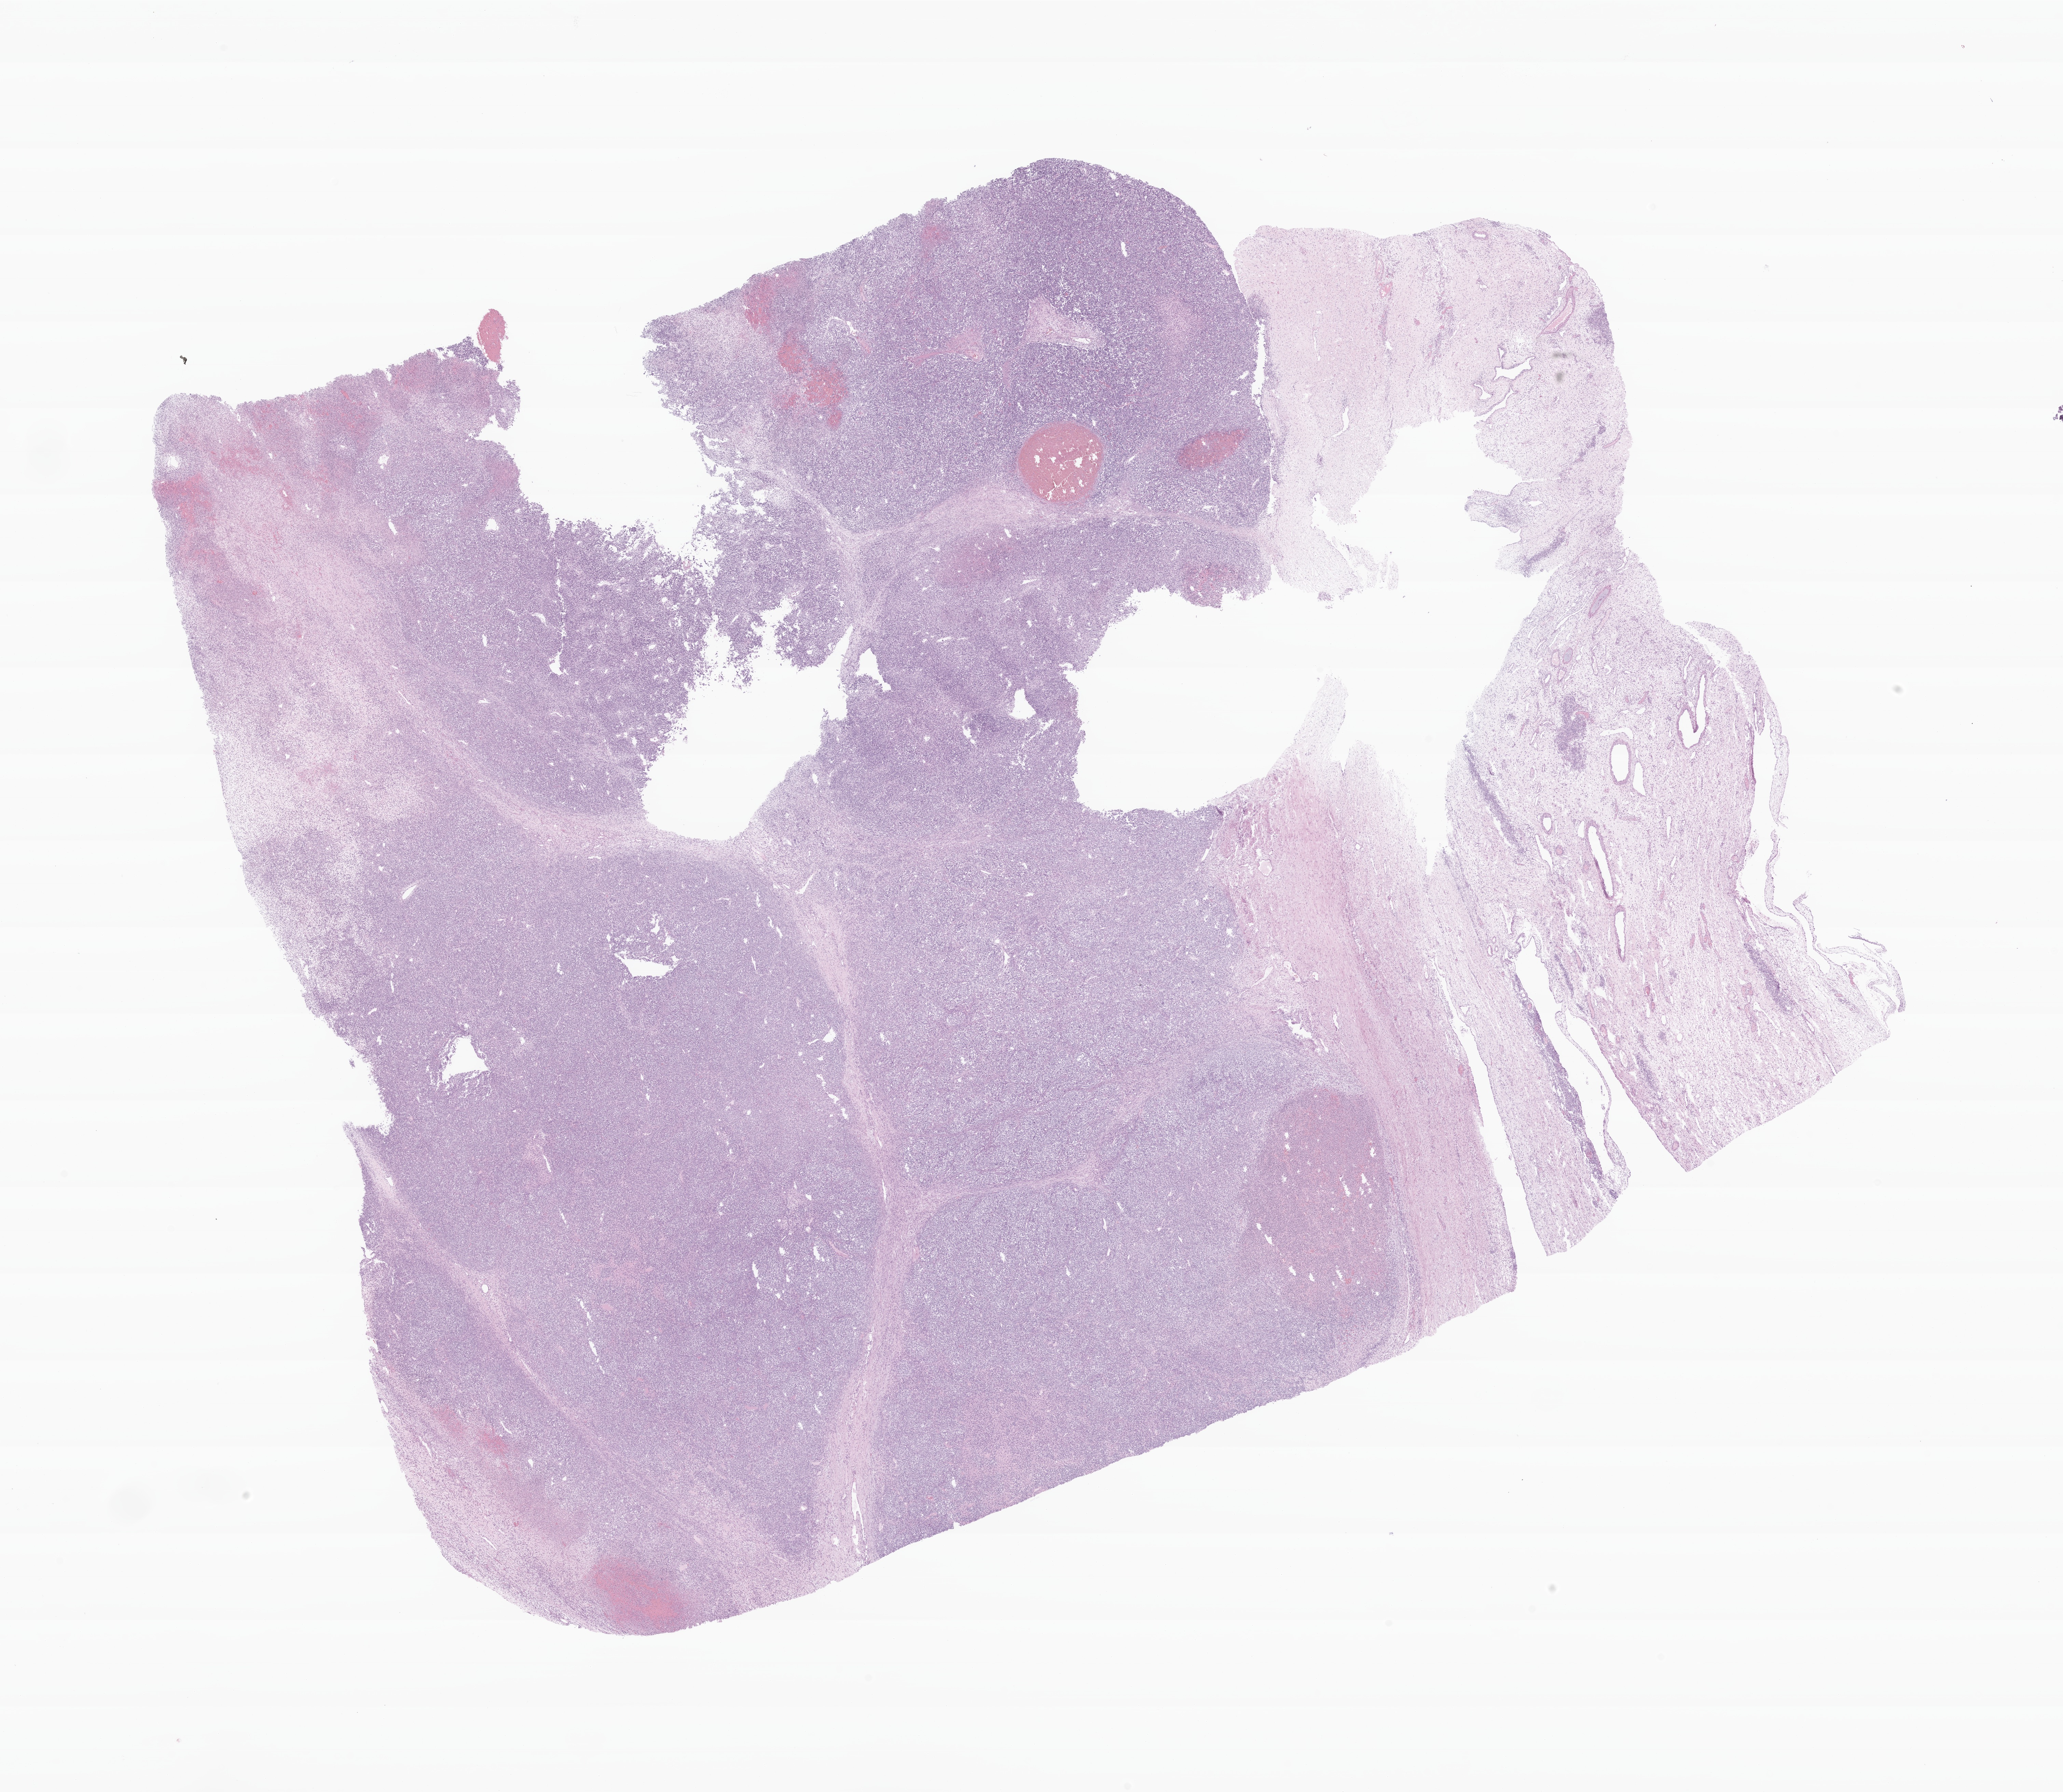
Whole-slide image, H&E stain of tumor tissue from the ovary, whole scanned area (about 25.4 x 22.1 mm) shown as a low-resolution overview; formalin-fixed paraffin-embedded section. Patient: female, age 179 months (14 years 11 months).
Recorded diagnosis: Sertoli-Leydig cell tumor, poorly diff, w. heterologous elements.